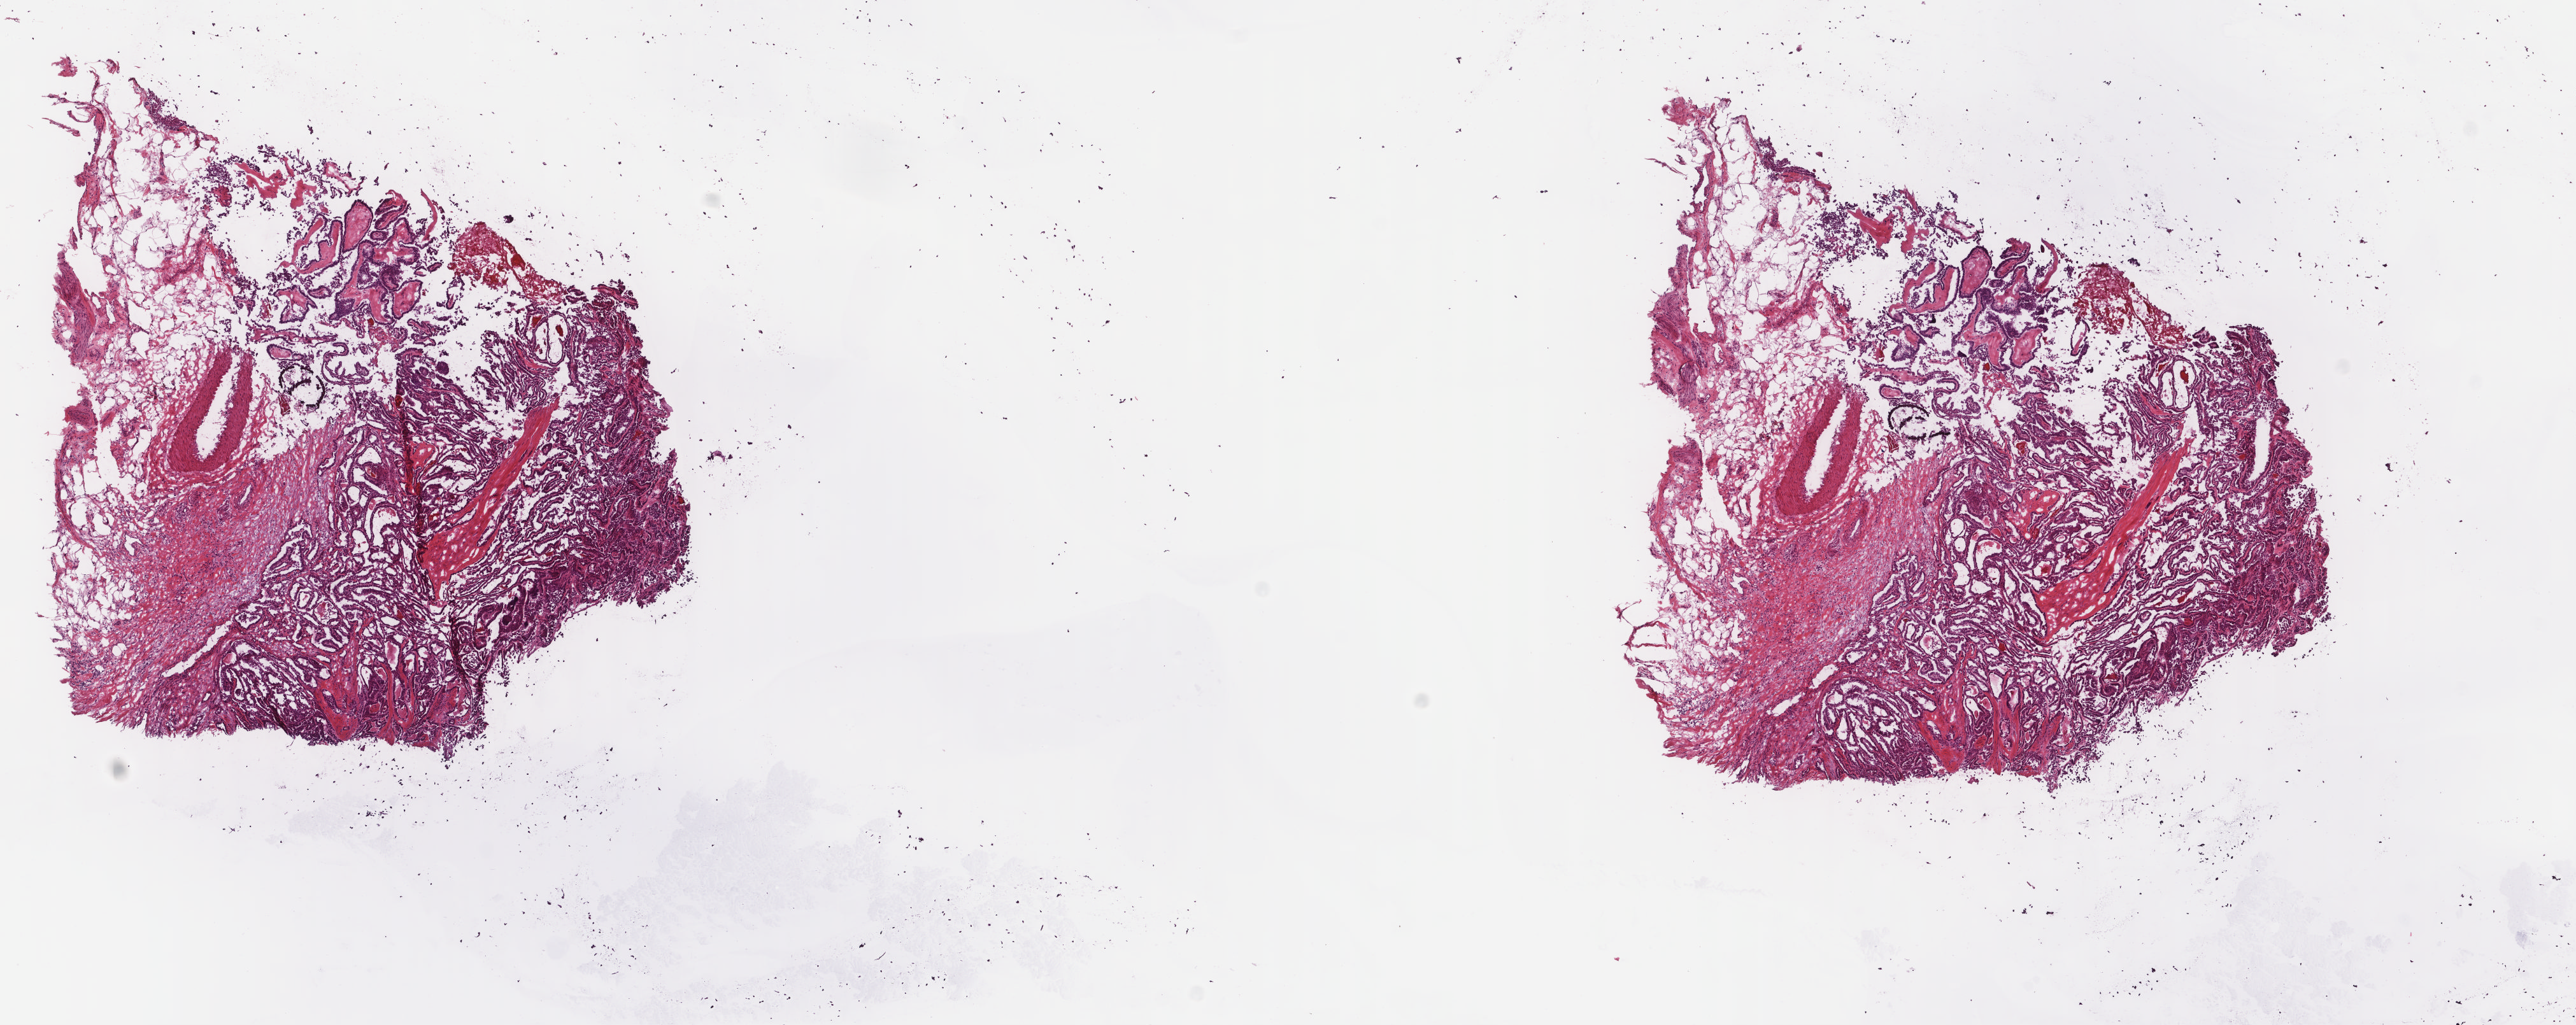
Digitized H&E-stained tissue section (whole slide) — low-resolution overview of the scanned area, about 16.1 x 6.4 mm. Frozen section. Thyroid, primary tumour sample. Male patient; age at initial diagnosis 56 years. Pathologist review of this section (percent, as recorded): tumour cells 65%, tumour nuclei 80%, normal cells 0%, stromal cells 35%, necrosis 0%. Inflammatory infiltration, as recorded: lymphocyte infiltration 0%, monocyte infiltration 0%, neutrophil infiltration 0%.
Pathologic diagnosis: Papillary carcinoma, columnar cell (thyroid gland). AJCC pathologic stage: IVA (7th edition).